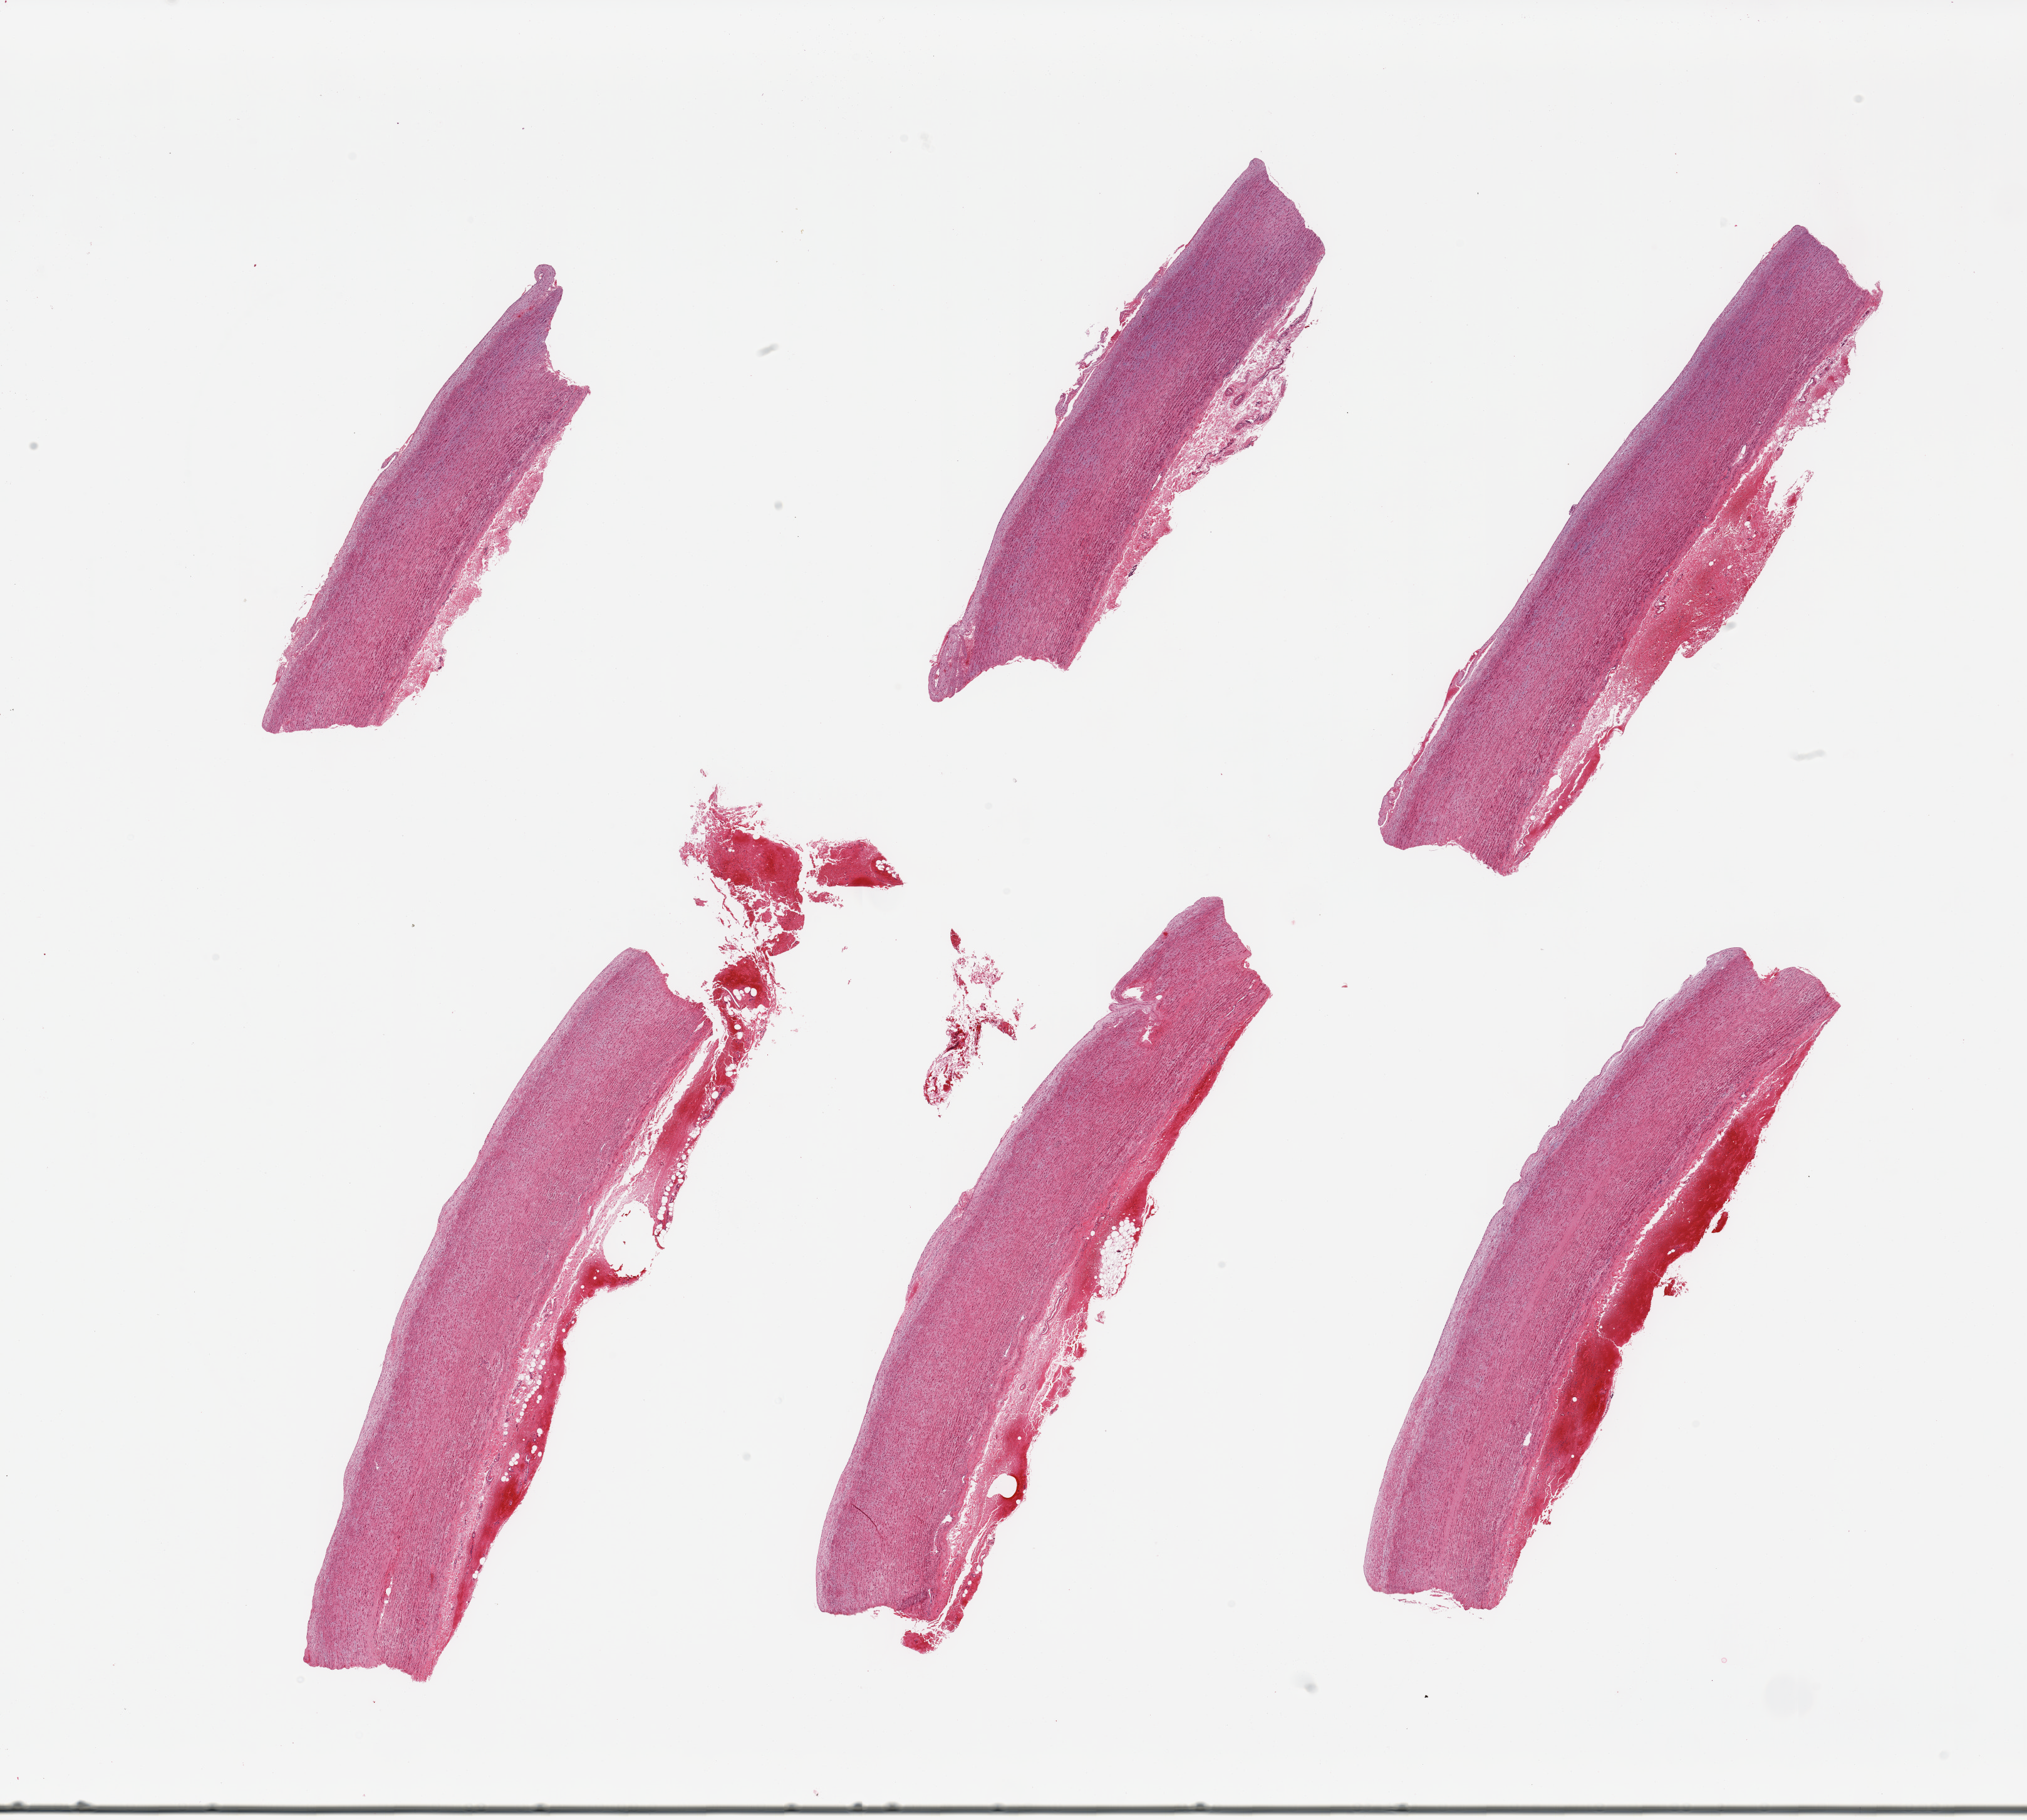
Haematoxylin and eosin whole-slide image — shown as a low-resolution overview of the whole scanned area (about 25.6 x 23.0 mm, acquisition: 20x scan). PAXgene-fixed, paraffin-embedded tissue. Sampled site (target tissue): aorta. Tissue donor sample. Male donor.
* pathologist's review note for this sample: 6 pieces; flat thin intimal thickening; hemorrhagic adventitia up to 0.9mm thick